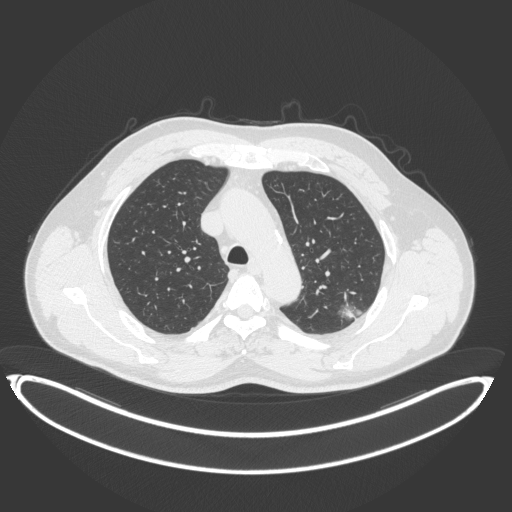
Chest CT, one axial slice; slice 268 of 399 in the series (ordered by position); lung window (W 1500 / L -600 HU); 512 × 512 image matrix, field of view 469 × 469 mm. Male patient, age 58 years. Case-level facts recorded for this patient, not image findings: clinical TNM (as recorded): T1c N0 M0.
Annotated regions visible in this slice (bounding box drawn by a radiologist):
- lung tumour (recorded histology: adenocarcinoma): box from (x=339, y=301) to (x=369, y=328) px